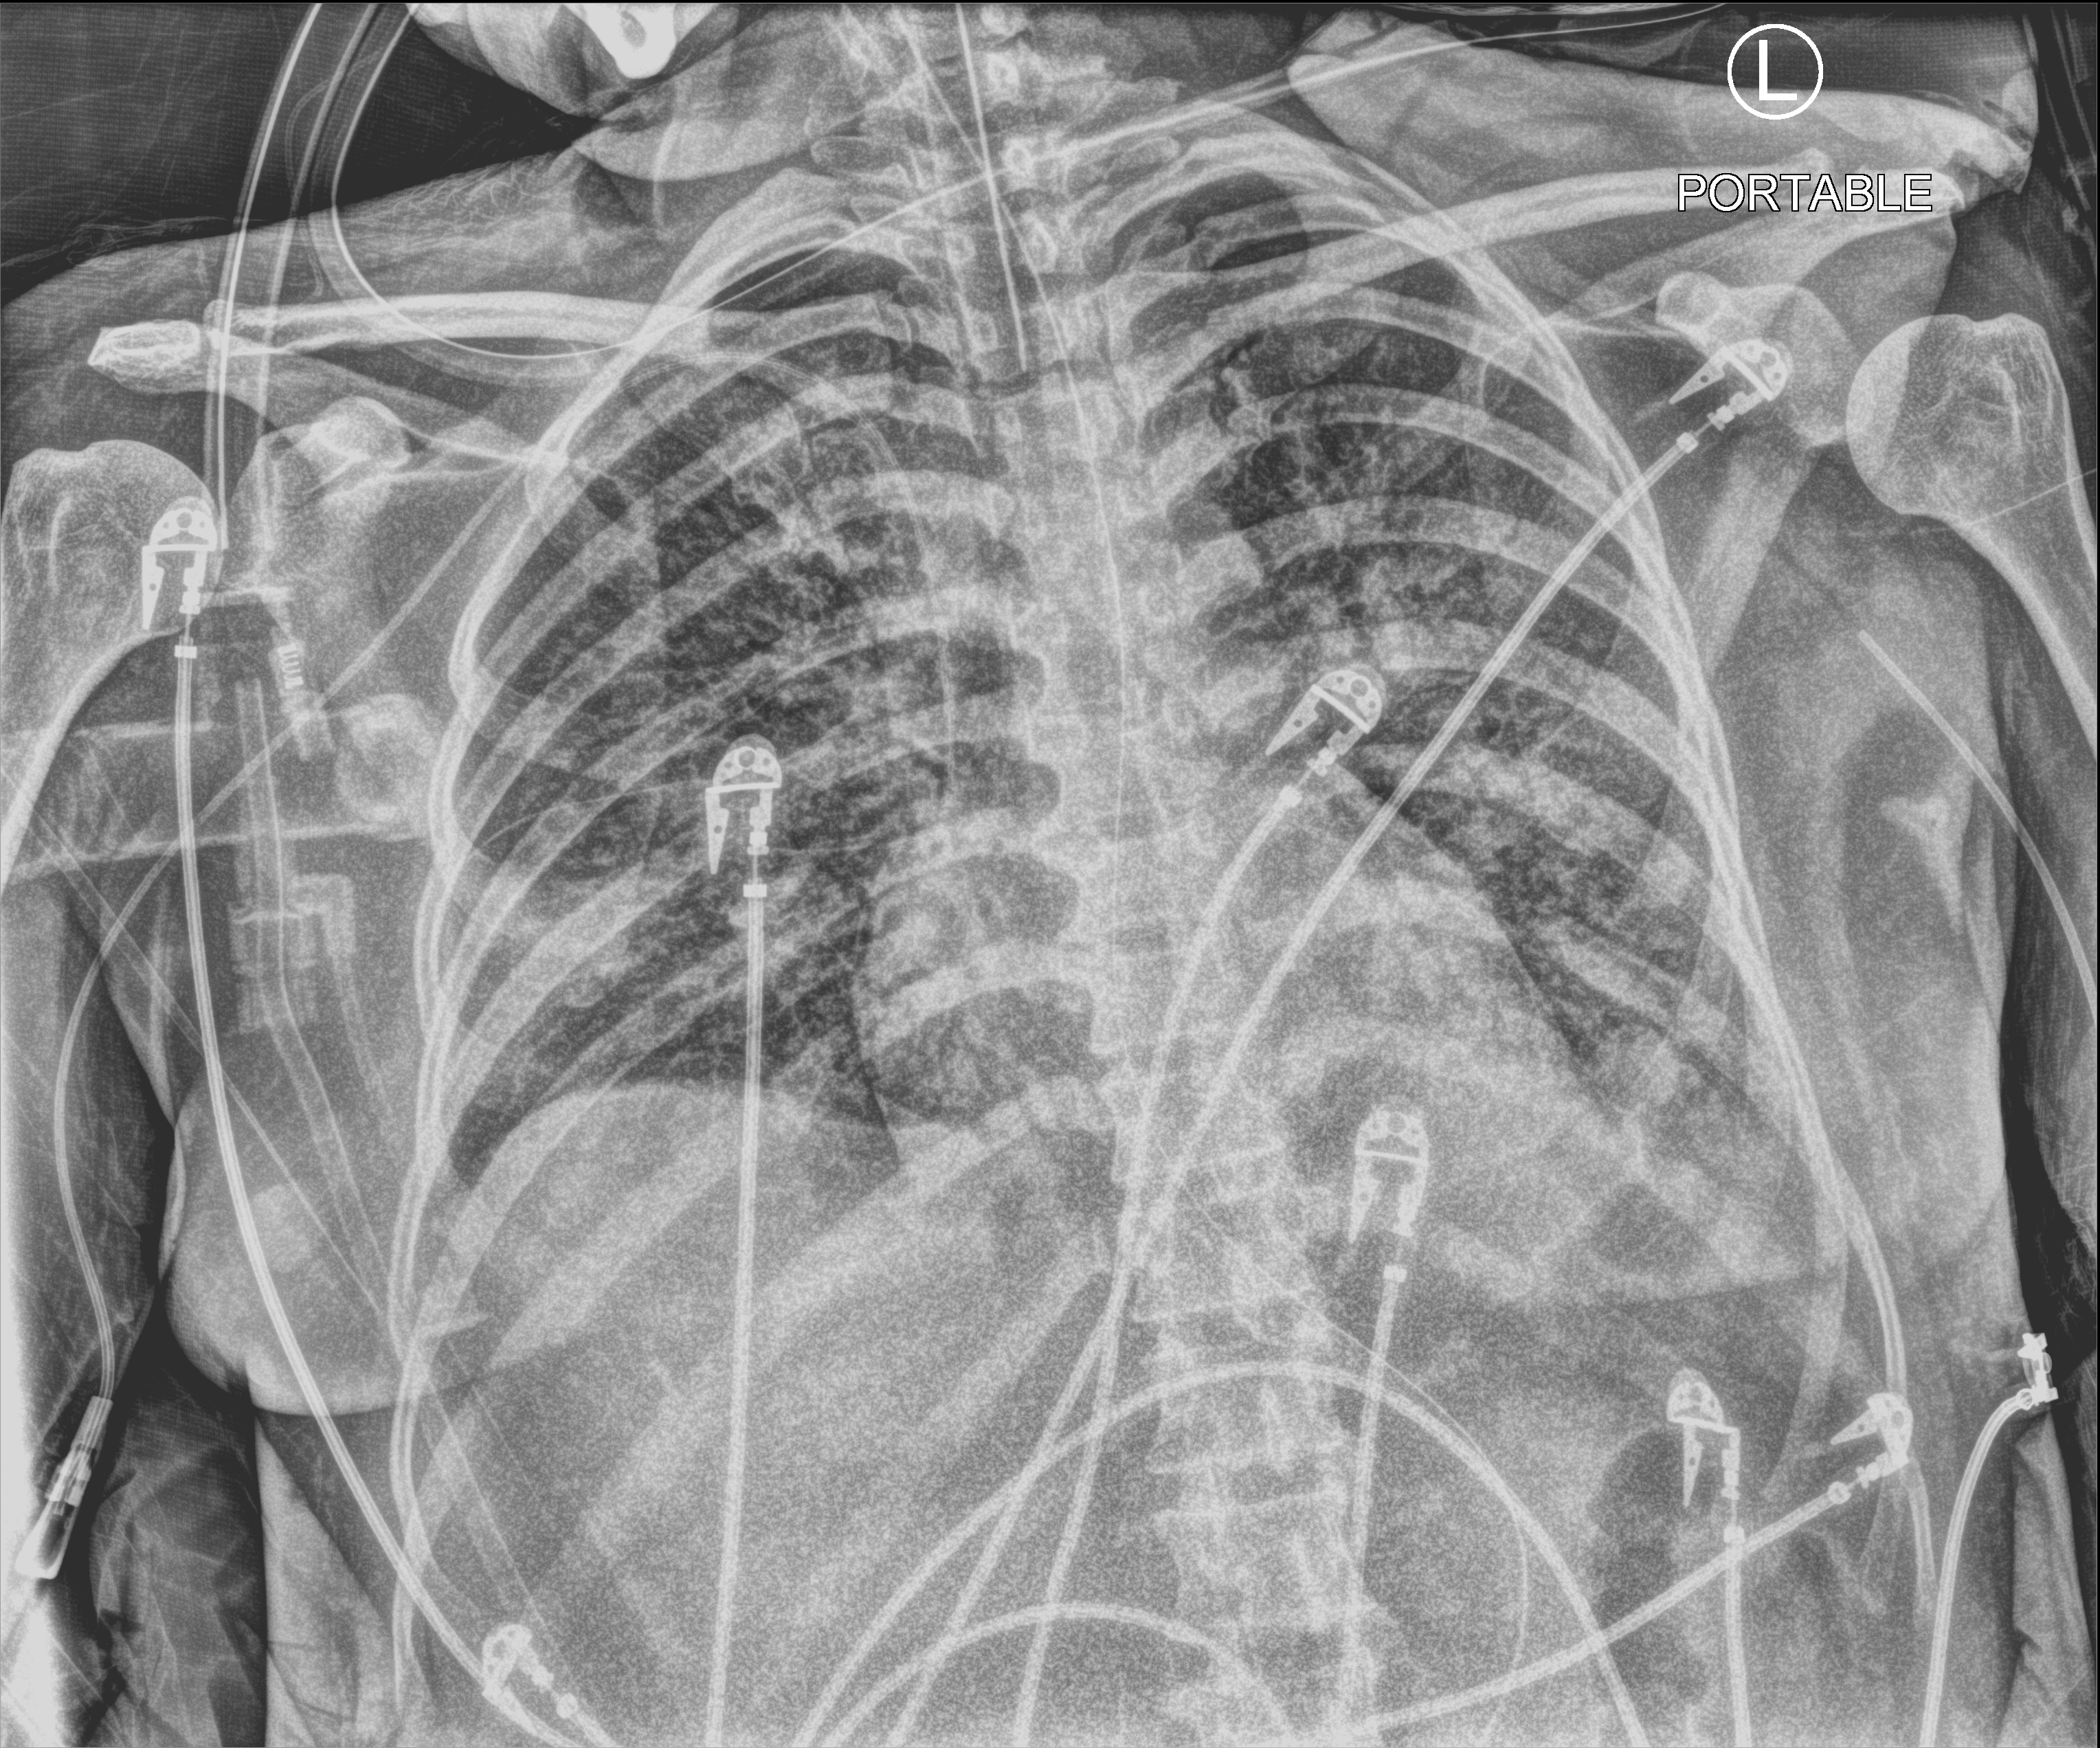
Bedside chest radiograph (computed radiography), anteroposterior (AP) projection. Patient hospitalised with COVID-19; female, aged 18–59 years.
From the hospital-stay record, not from the radiograph (when in the stay this image was taken is not recorded): chronic kidney disease (admission record): no; diabetes (admission record): no.